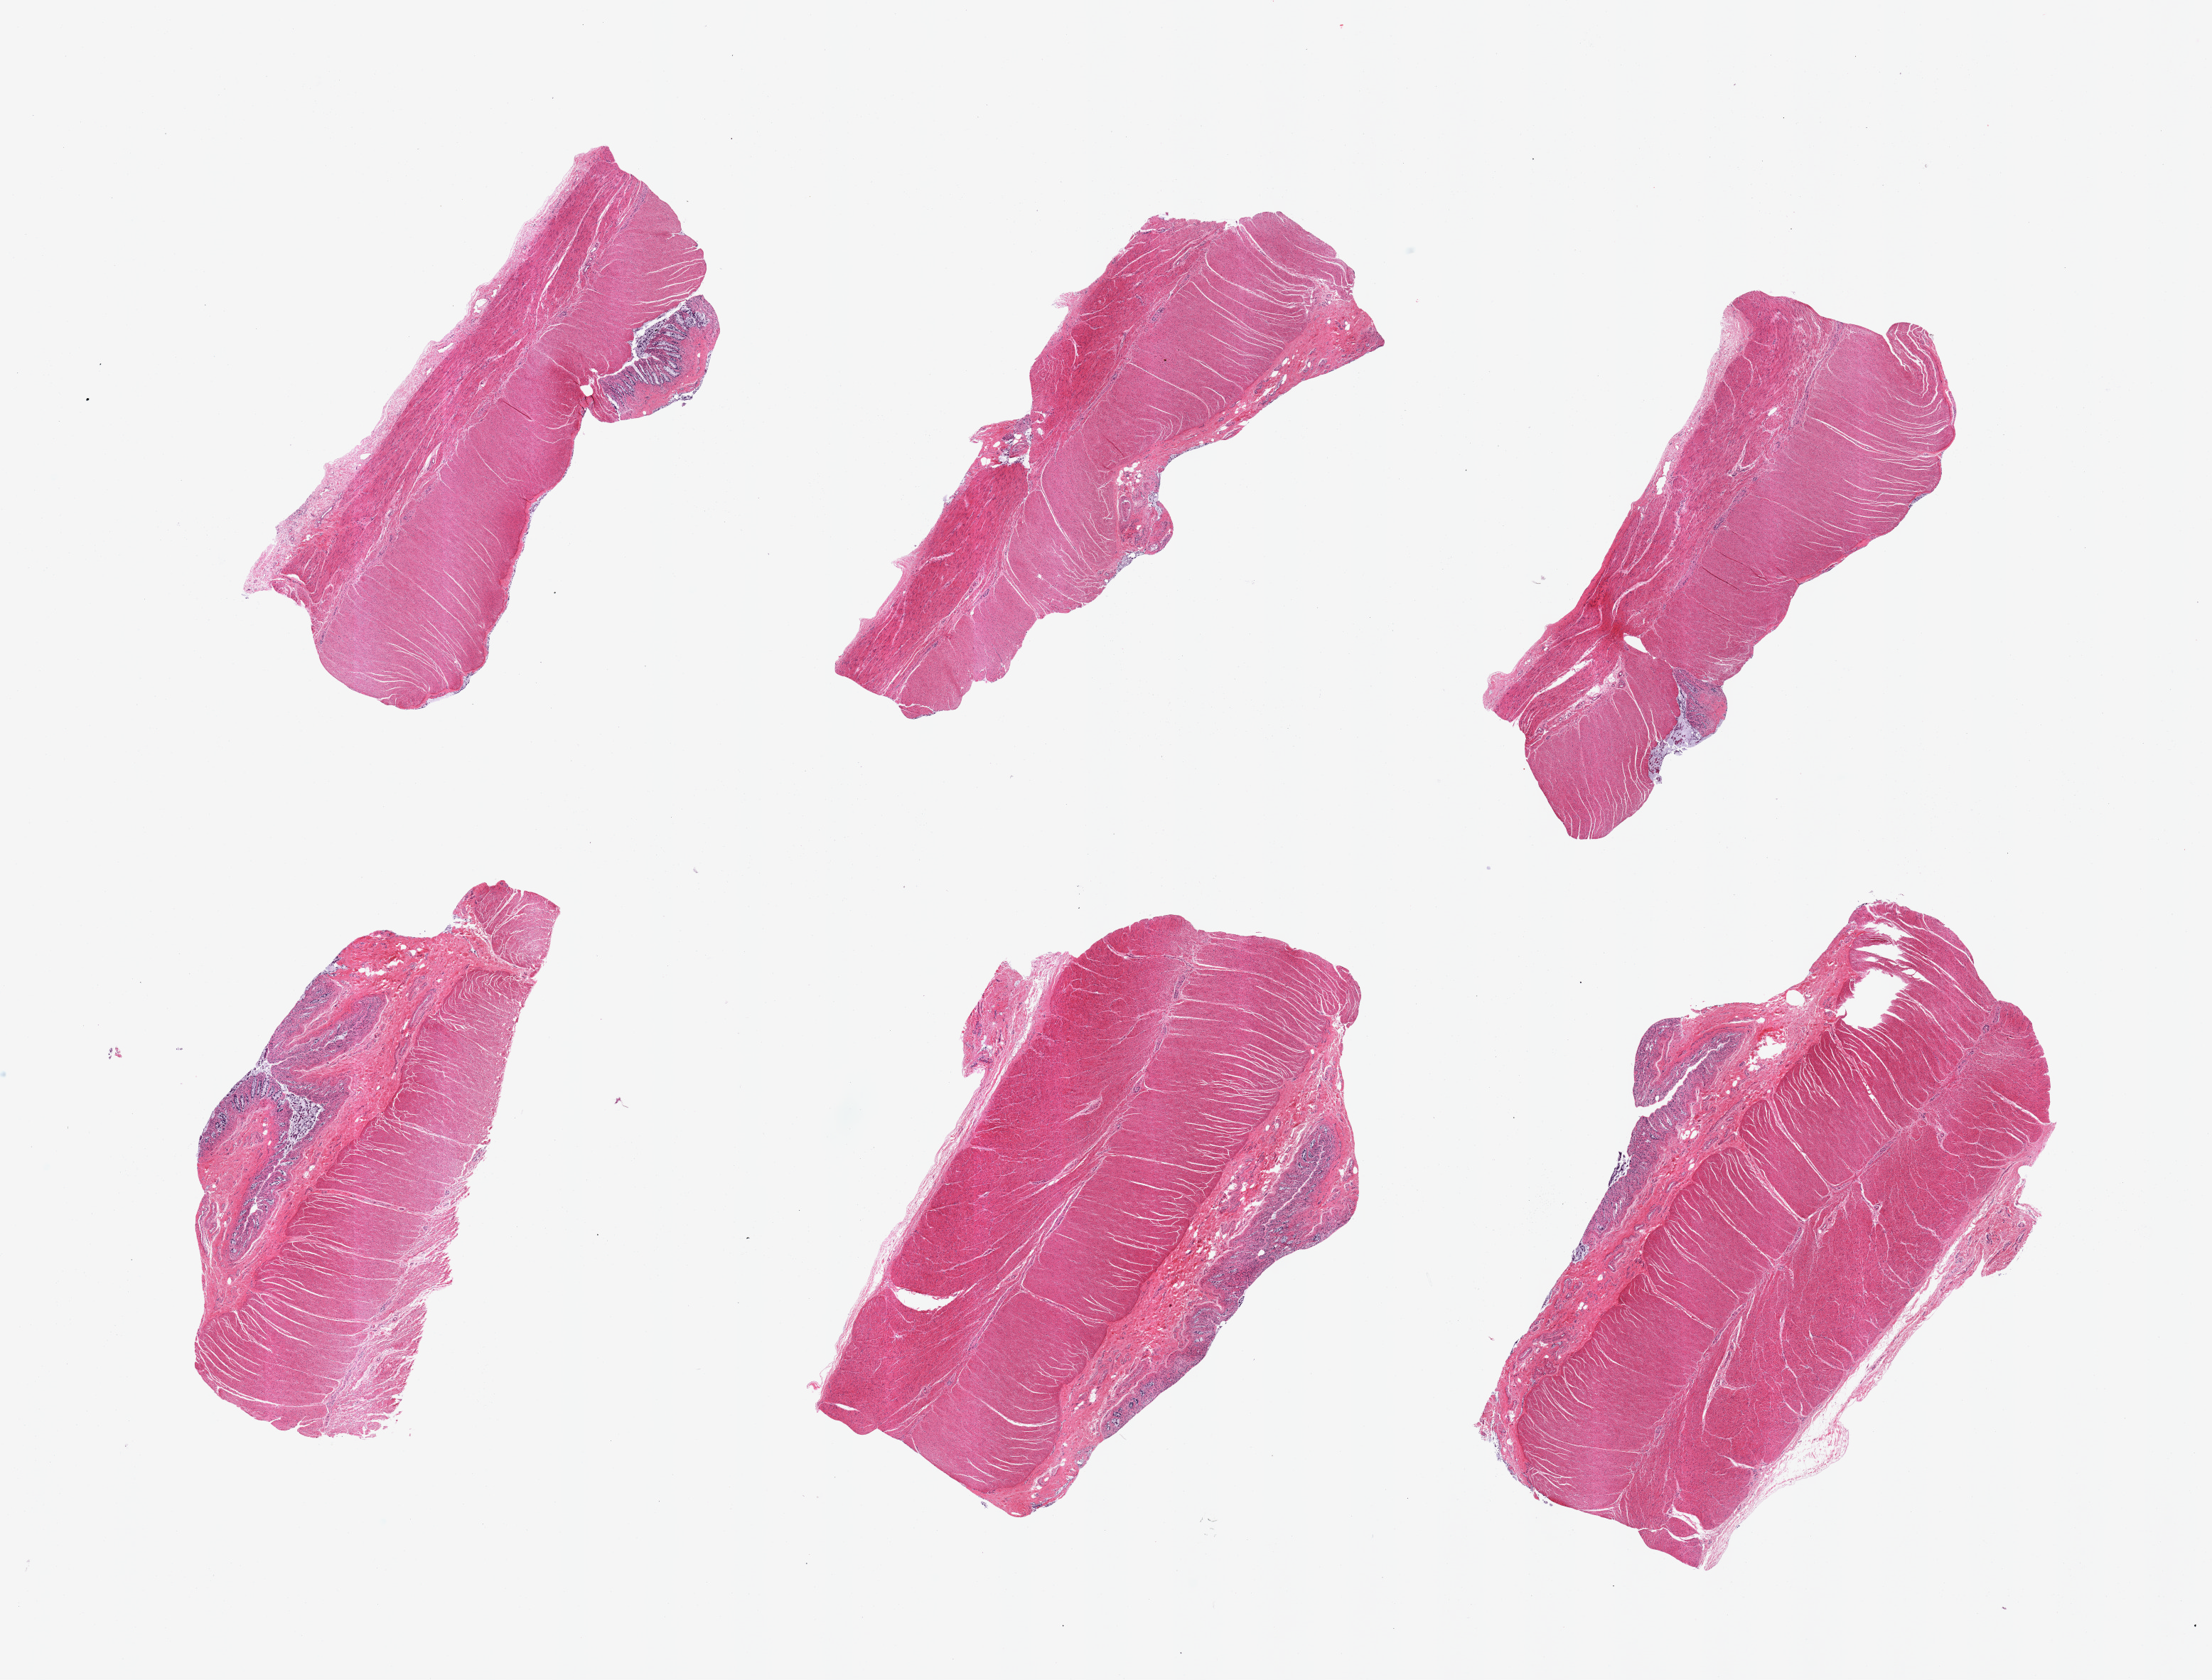
H&E whole-slide image, low-resolution overview of the scanned area, about 24.6 x 18.7 mm, PAXgene-fixed paraffin-embedded (PFPE) section, sampled site (target tissue): sigmoid colon, tissue donor sample.
Pathologist's review note for this sample: 6 pieces, confirmed target muscularis.